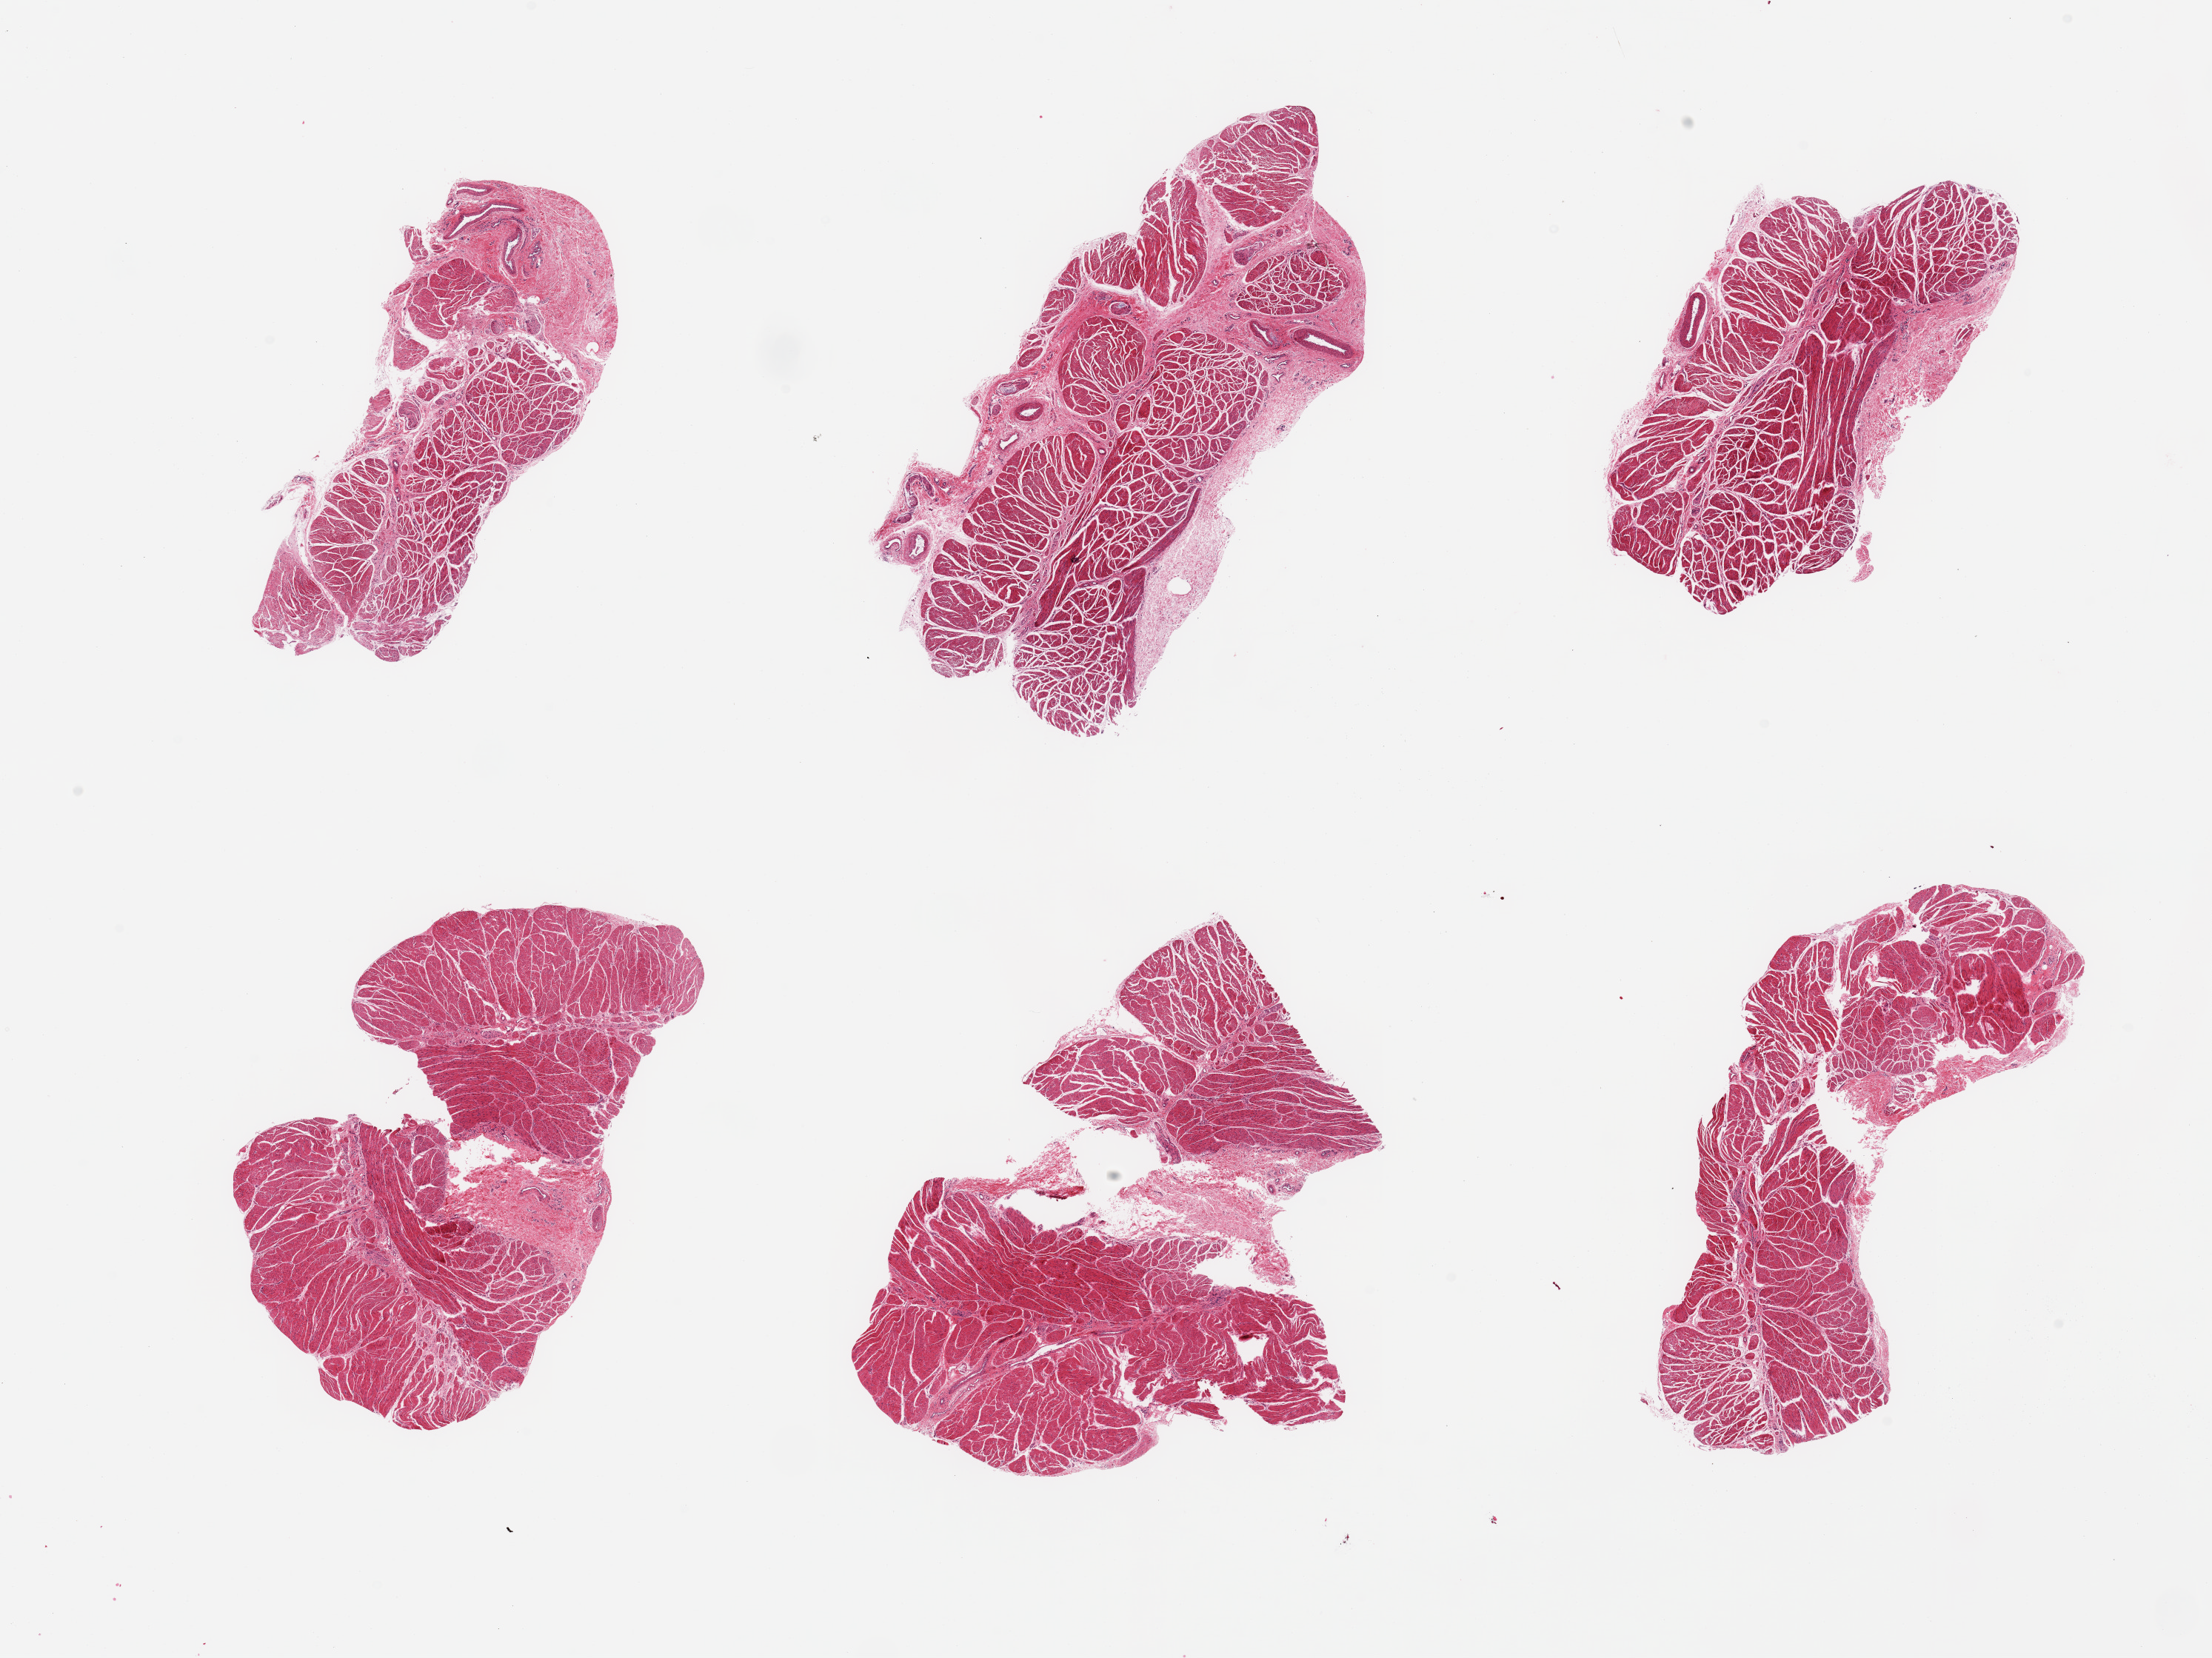
Digitized haematoxylin and eosin-stained section — shown as a low-resolution overview of the whole scanned area (about 23.6 x 17.7 mm, slide scanned at 20x), PAXgene-fixed paraffin-embedded (PFPE) section, section of esophageal muscle (target tissue), donor tissue sample.
Pathologist's review note for this sample: 6 pieces, confirmed target muscularis.